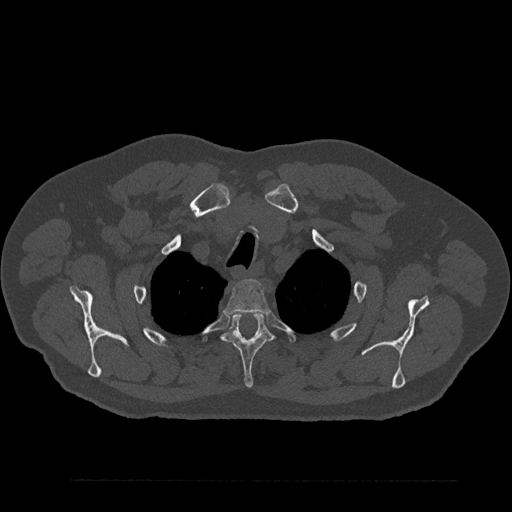
CT including the spine, one axial slice; position 690 of 797 along the scan axis; 120 kVp; bone window (W 1800 / L 400 HU); 0.5 mm slice thickness; 512 × 512 image matrix. Male patient, age 61 years. Case-level facts recorded for this patient, not image findings: primary cancer: prostate.
Annotated regions visible in this slice (semi-automatically segmented with operator editing):
- T2 vertebra: bounding box <225,279,269,314> (left, top, right, bottom; pixels)
- T3 vertebra: <222,312,273,388>